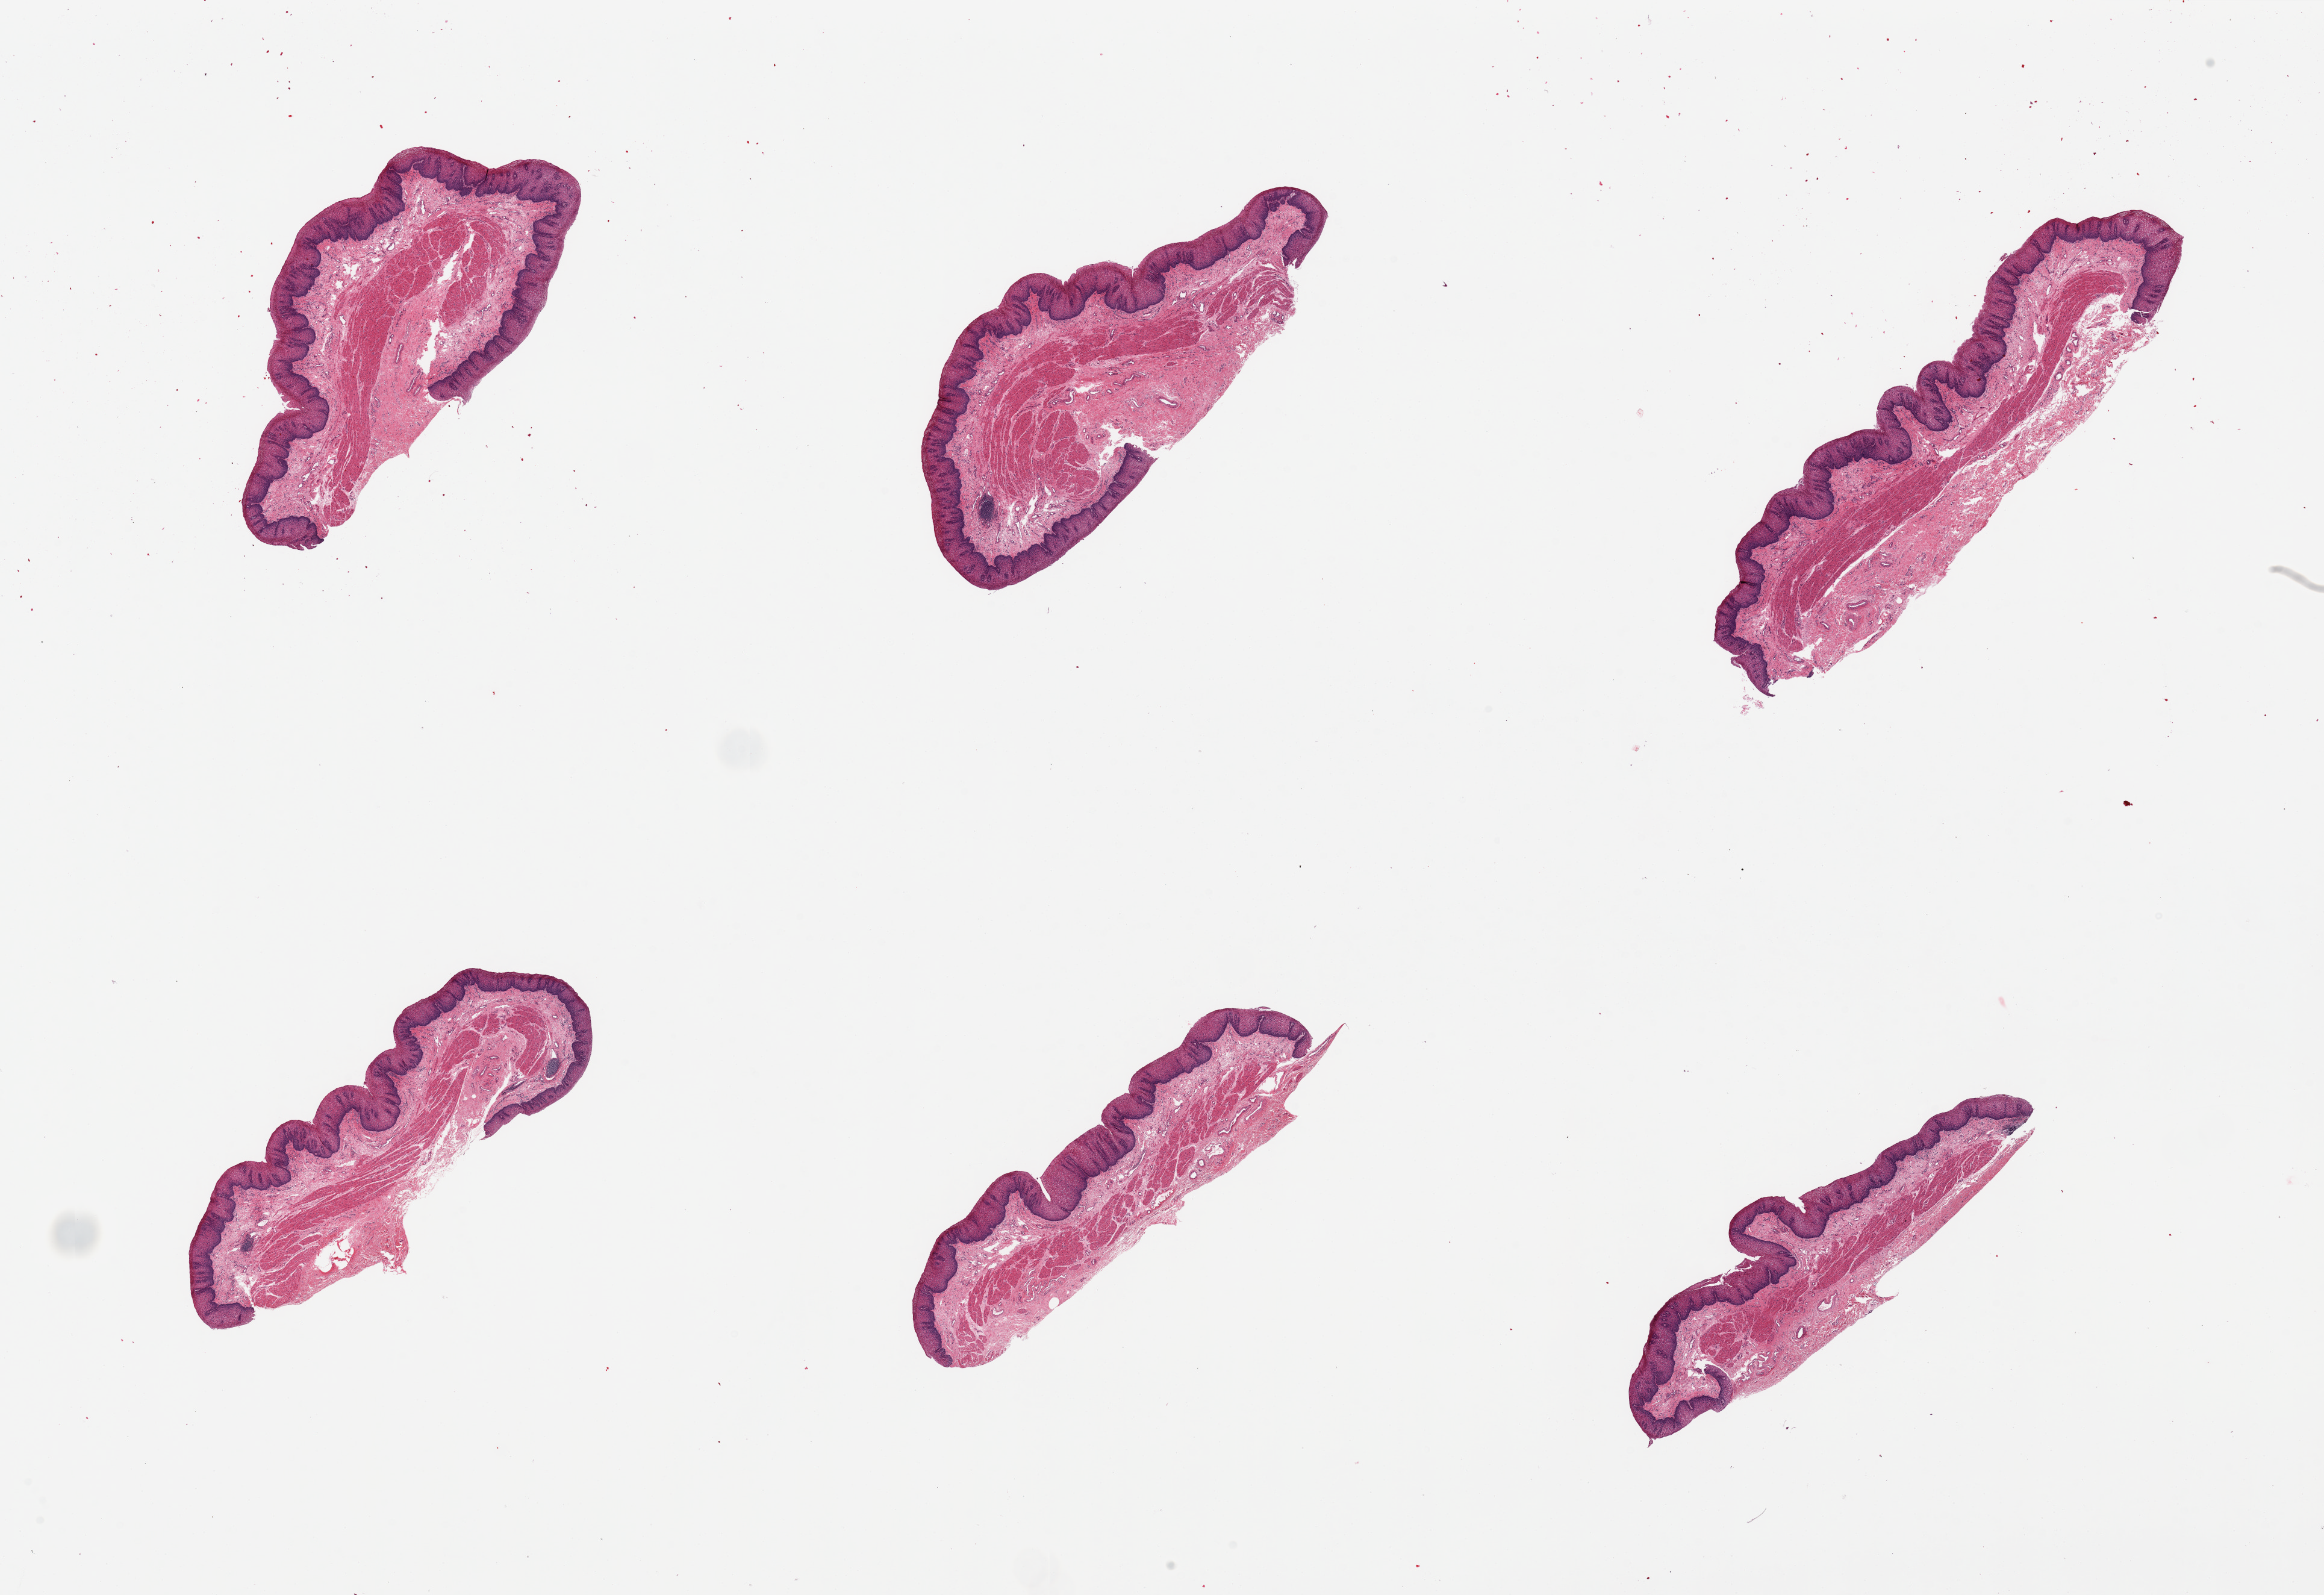
Whole-slide image, H&E stain — low-resolution overview of the scanned area, about 30.5 x 20.9 mm, PAXgene-fixed paraffin-embedded (PFPE) section, target tissue: esophageal mucous membrane, donor tissue sample.
* pathologist's review note for this sample: 6 pieces. Well dissected